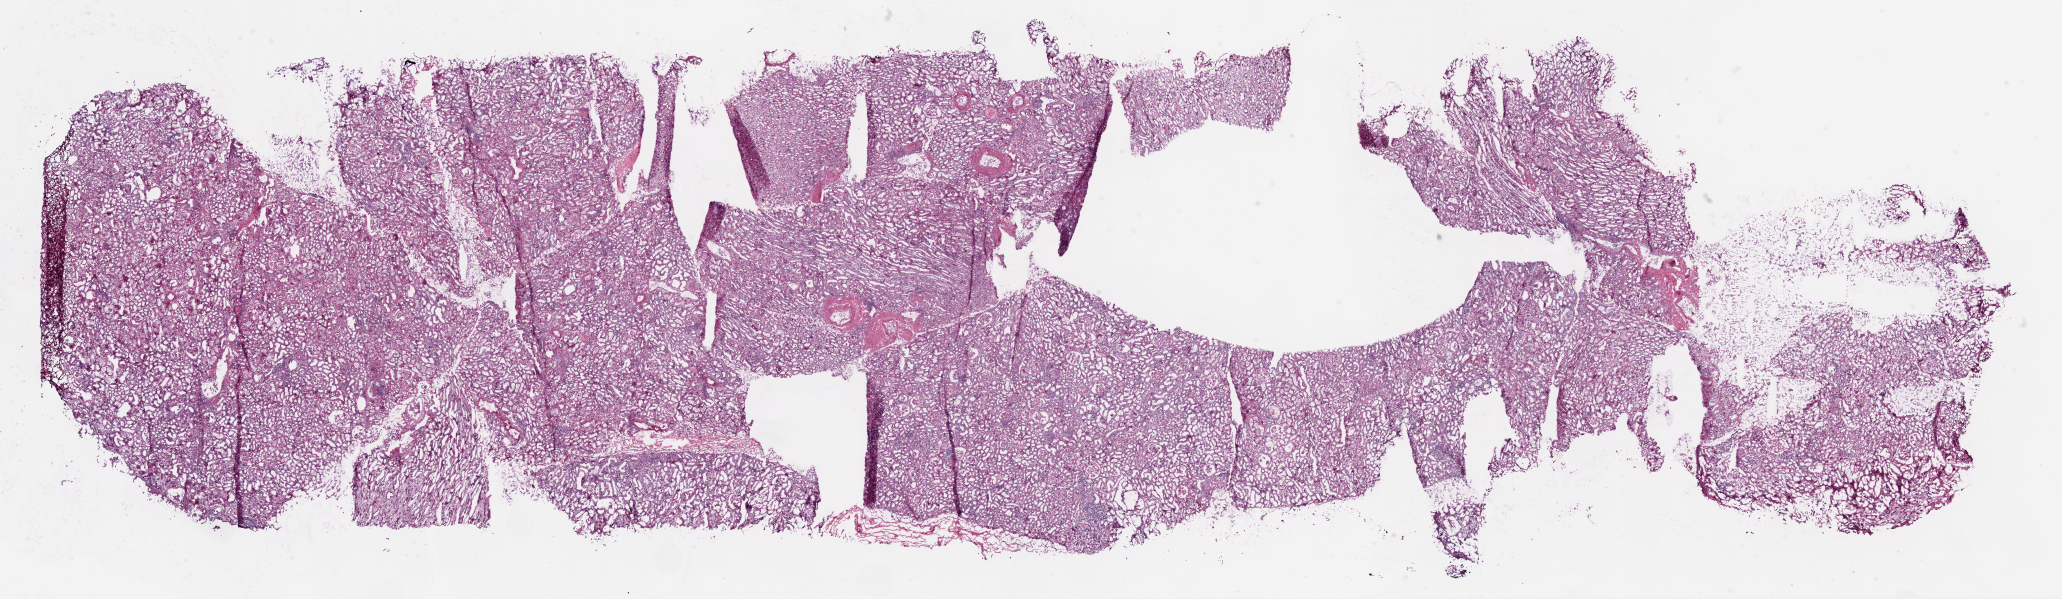
Whole-slide histology image, H&E-stained — low-resolution overview of the scanned area, about 33.1 x 9.6 mm (acquisition: 20x scan). Frozen section. Solid tissue normal (non-tumour tissue) sample from the kidney. Male patient; age at initial diagnosis 48 years.
This section: solid tissue normal (non-tumour) sample from the same patient. Patient diagnosis: Clear cell adenocarcinoma, NOS.